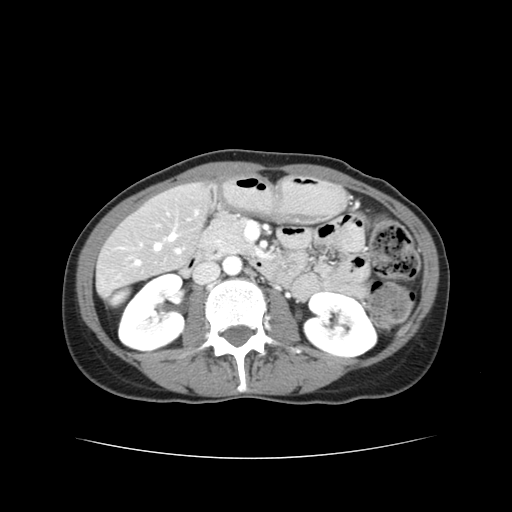
Contrast-enhanced abdominal CT, one axial slice. Slice 13 of 38 in the series (ordered by position). 120 kVp. Intravenous contrast given. Soft-tissue window (W 400 / L 40 HU). 5 mm slice thickness. 512 × 512 image matrix, field of view 340 × 340 mm. Female patient, age 54 years. Case-level facts recorded for this patient, not image findings: diagnosis: colorectal cancer liver metastases, imaged before liver resection; multiple liver metastases: yes; largest metastasis: 1.1 cm; disease in both lobes: yes.
Outlined on this slice (outlined manually by an expert reader):
- hepatic veins: box from (x=155, y=234) to (x=177, y=250) px
- liver: (x=96, y=184)–(x=206, y=291)
- portal vein (with intrahepatic branches): (x=136, y=250)–(x=180, y=265)